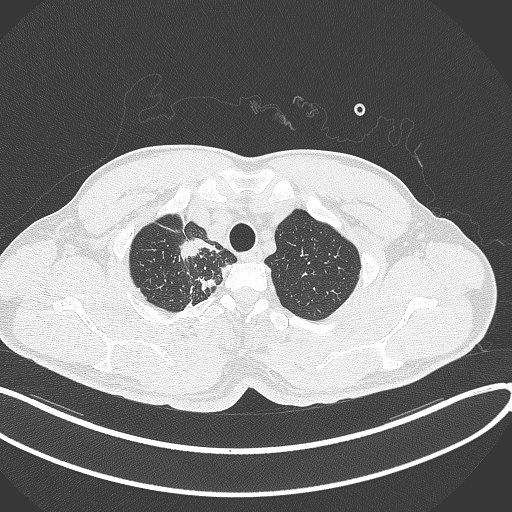
Chest CT, one axial slice. Position 332 of 391 along the scan axis. Reconstruction kernel B70f. Lung window (W 1500 / L -600 HU). 1 mm slice thickness. 512 × 512 image matrix, field of view 400 × 400 mm. Male patient, age 48 years. From the clinical record (not read from this slice): clinical TNM (as recorded): T1c N1 M1.
Annotated regions visible in this slice (bounding box drawn by a radiologist):
- lung tumour (recorded histology: adenocarcinoma): bounding box (x1, y1, x2, y2) in pixels: (176, 236, 205, 264)